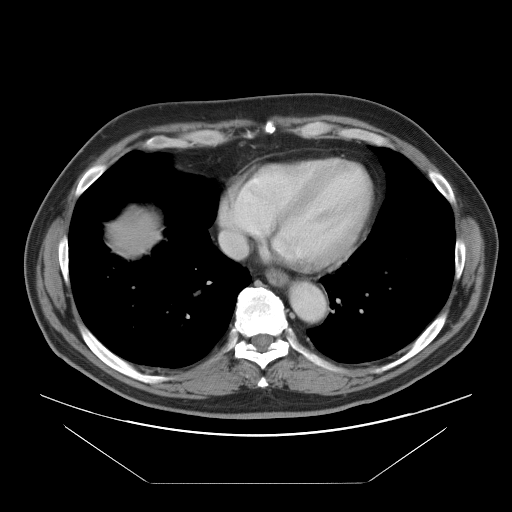
Contrast-enhanced abdominal CT, one axial slice; slice 91 of 97 in the series (ordered by position); 120 kVp; intravenous contrast given; soft-tissue window (W 400 / L 40 HU); 512 × 512 image matrix. Male patient, age 62 years. Case-level facts recorded for this patient, not image findings: diagnosis: colorectal cancer liver metastases, imaged before liver resection; multiple liver metastases: no; largest metastasis: 7 cm; chemotherapy before resection: yes.
Structures marked on this image (manually delineated by an expert):
- hepatic veins: bounding box (x1, y1, x2, y2) in pixels: (221, 188, 247, 259)
- liver: (119, 221, 148, 244)
- planned liver remnant (the part of the liver to remain after resection): (118, 221, 149, 243)